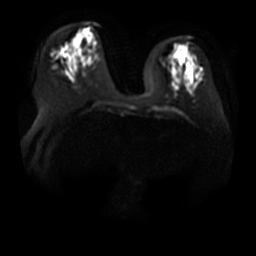
Breast MRI, one axial slice. Slice 14 of 36 in the series (ordered by position). Diffusion-weighted series; image 2 of 4 stored at this slice position (different b-values; order by instance number). 3 T. 5 mm slice thickness. 256 × 256 image matrix, field of view 380 × 380 mm. Female patient.
Outlined on this slice (expert manual segmentation):
- tumour on diffusion-weighted imaging: box from (x=73, y=37) to (x=80, y=46) px